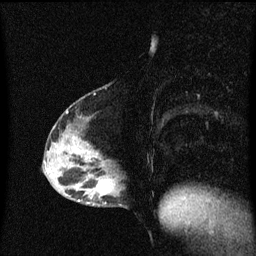
Breast MRI (dynamic contrast-enhanced), one sagittal slice; slice 25 of 60 in the series (ordered by position); dynamic contrast-enhanced series, image 2 of 3 at this slice position (ordered by acquisition); 1.5 T; TE 4.2 ms, TR 8.4 ms; 256 × 256 image matrix. Patient: female, 40 years.
Structures marked on this image (semi-automatic segmentation, software-assisted and operator-edited):
- analysis volume of interest (the breast-tissue region the enhancement analysis was run in; not a lesion): bounding box [x1, y1, x2, y2] px = [82, 172, 128, 209]
- tumour enhancement mask (voxels above the 70 % enhancement threshold inside the analysis volume of interest): [89, 194, 95, 205]